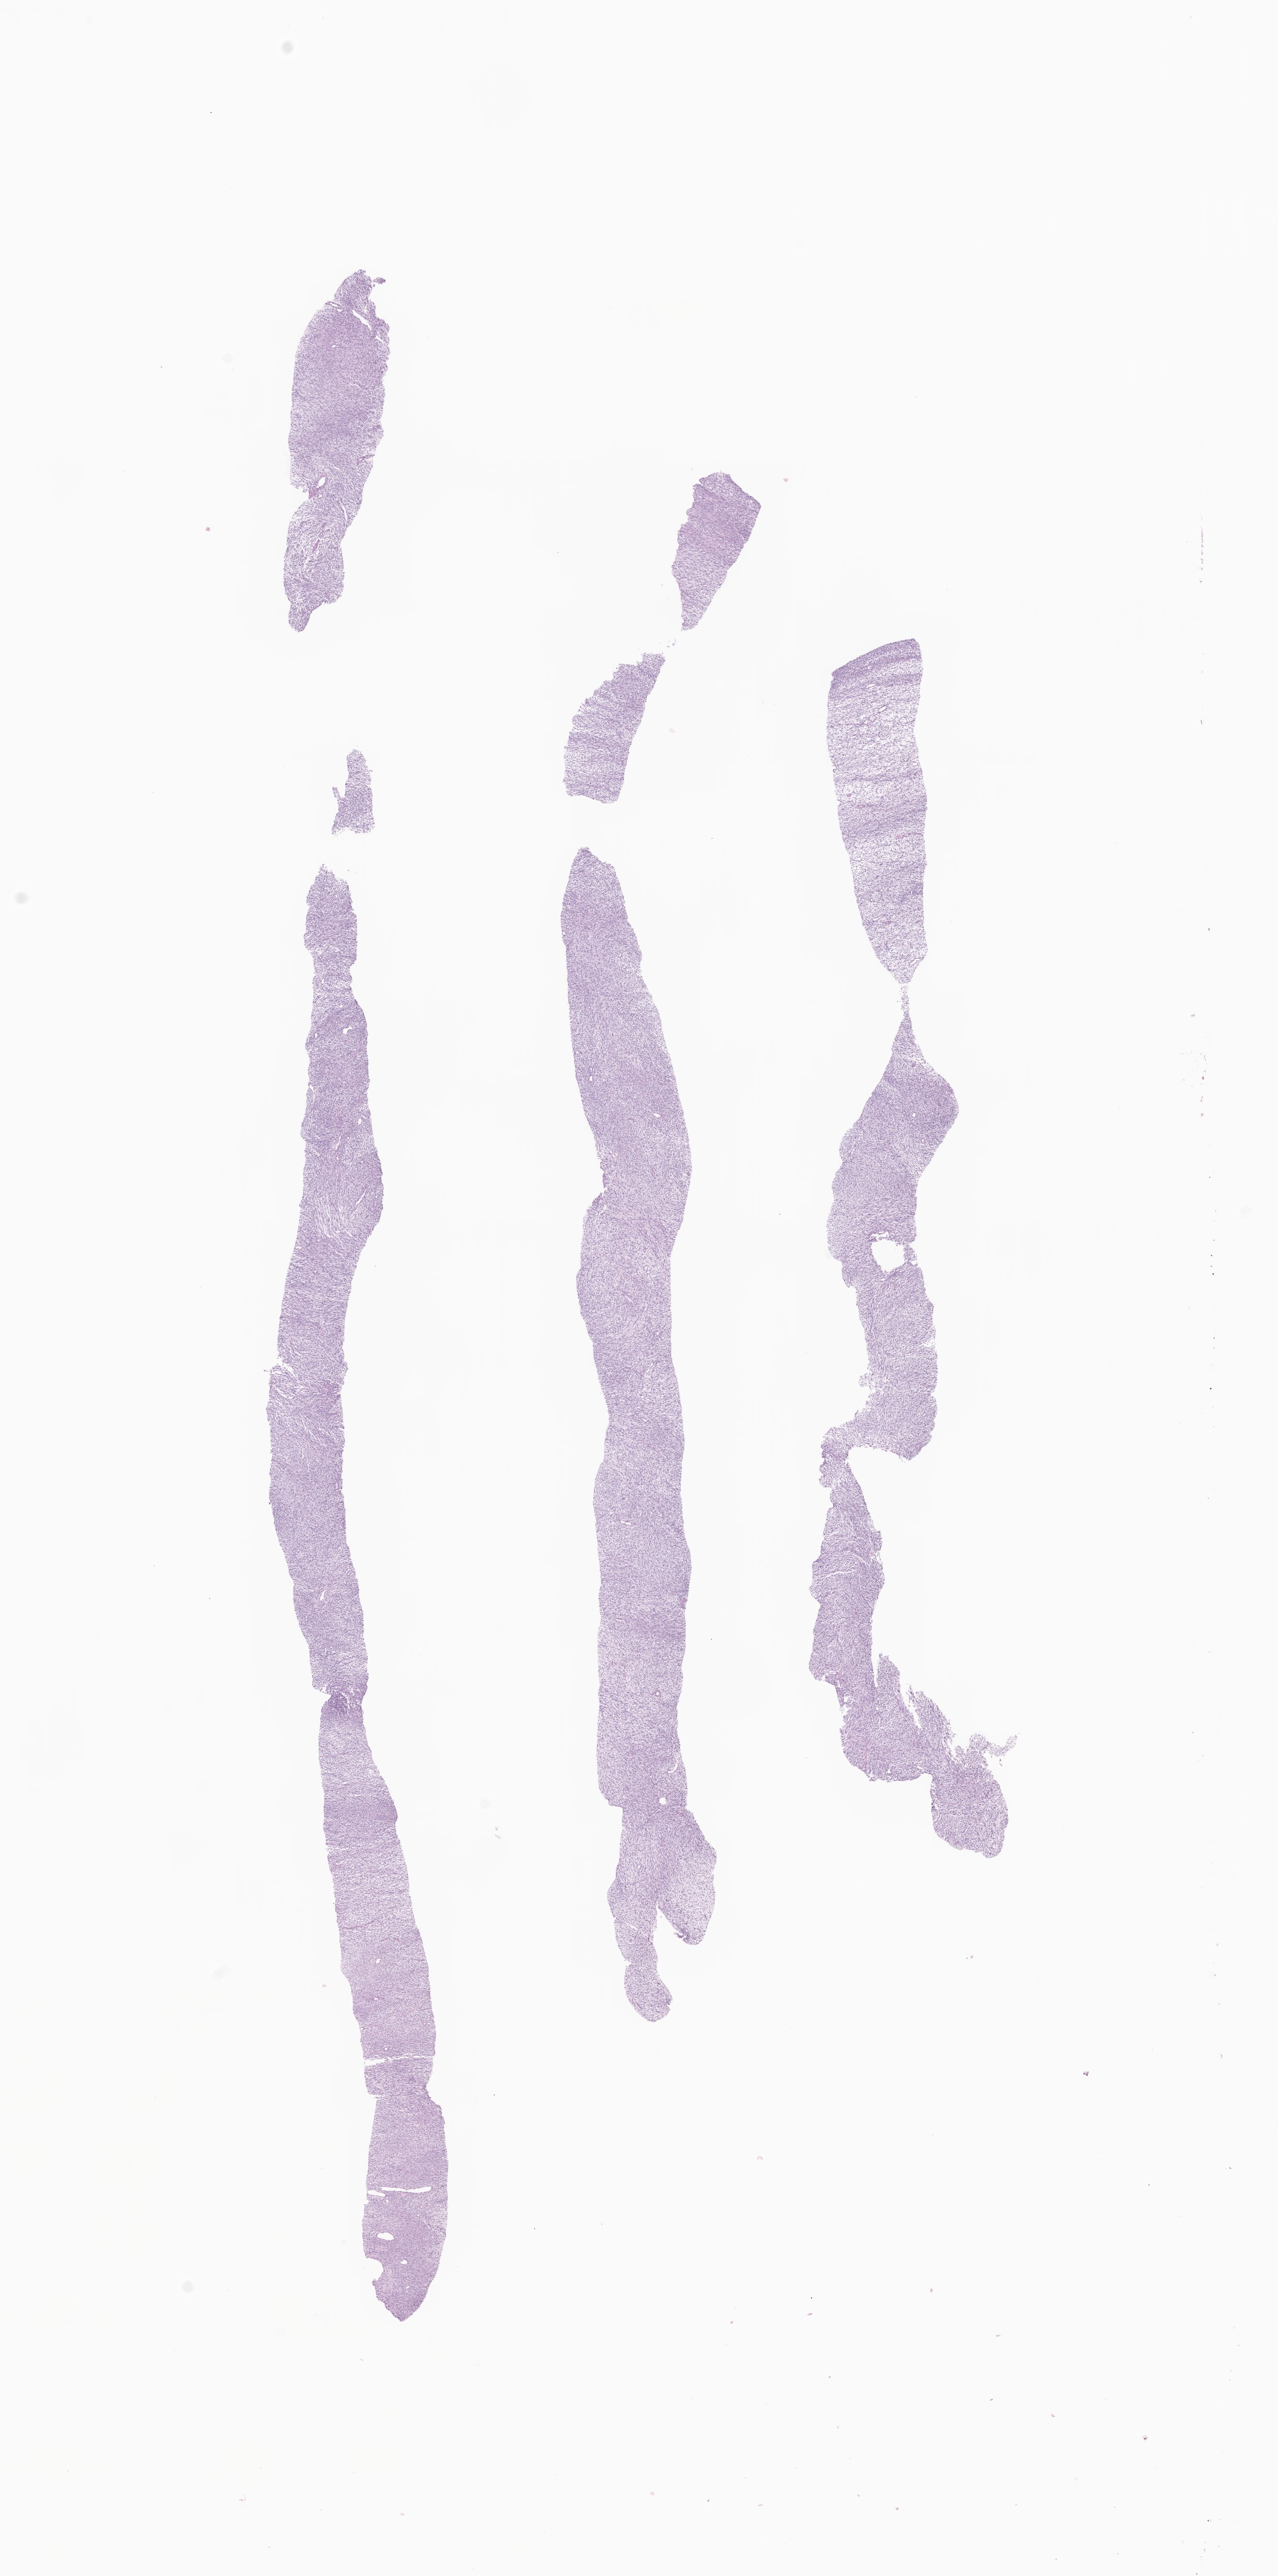
Digitized H&E-stained section of tumor tissue from the pelvis, low-resolution overview of the scanned area, about 9.0 x 18.2 mm. Formalin-fixed paraffin-embedded section. Patient: female, age 153 months (12 years 9 months).
Diagnosis: Synovial sarcoma, NOS.